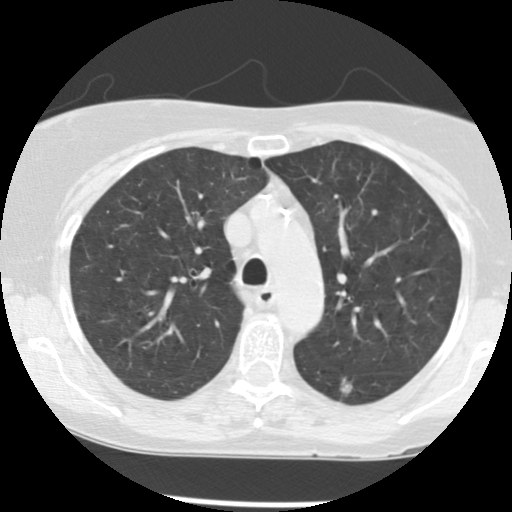
Chest CT (low-dose screening protocol), one axial image; second screening round (one year after baseline); lung window (W 1500 / L -600 HU); 2.5 mm slice thickness; 120 kVp; slice 33 of 124 in the series. Female, age 63 years at enrolment. Current smoker at enrolment.
Expert reader's lesion annotation, bounding box [x1, y1, x2, y2] px = [327, 370, 369, 405]. The exam's reader record, not a measurement of the box and not confirmed to be the same lesion: non-calcified nodule or mass ≥4 mm, left lower lobe, 7 × 6 mm, poorly defined margins, soft tissue attenuation, pre-existing on the prior screen: yes; interval growth: yes. Official screen result: positive, other. Lung cancer was diagnosed 460 days after this screen: squamous cell carcinoma, NOS, left lower lobe, moderately differentiated (G2), stage IB (AJCC 6th edition), 15 mm at pathology.